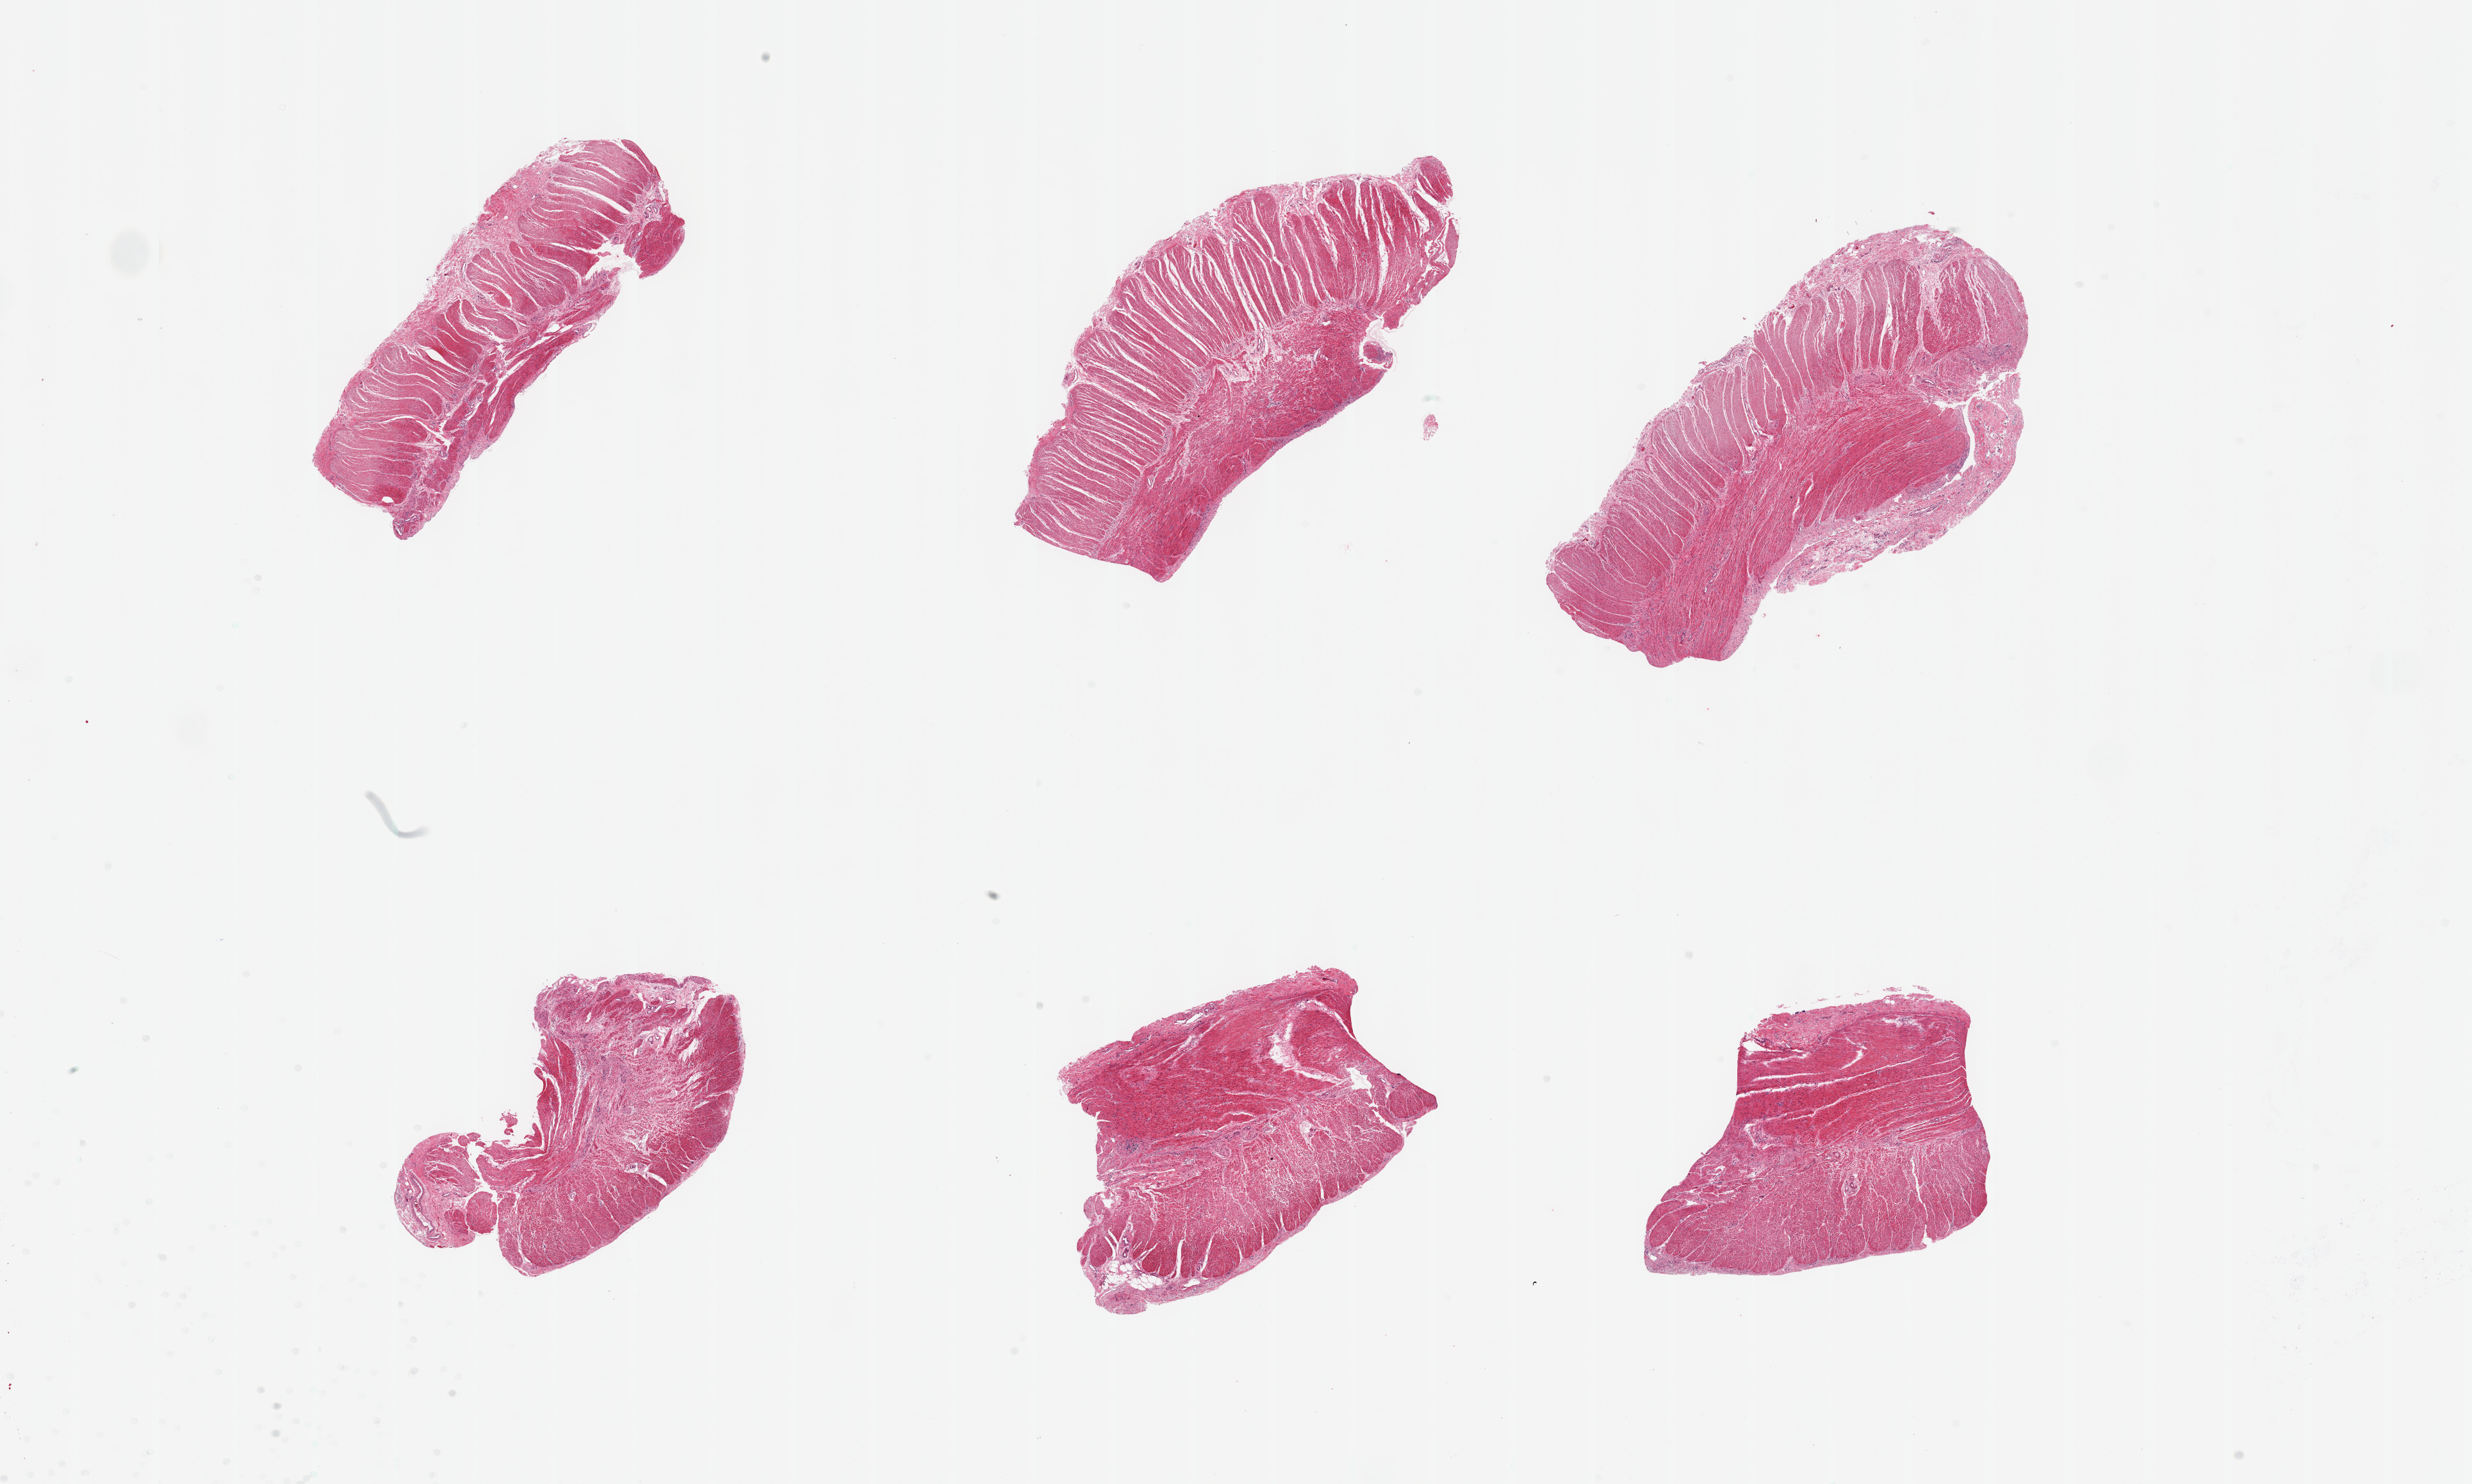
Digitized hematoxylin and eosin (H&E)-stained section — shown as a low-resolution overview of the whole scanned area (about 30.5 x 18.3 mm), PAXgene-fixed, paraffin-embedded tissue, sampled site (target tissue): sigmoid colon, donor tissue sample.
• reviewer comment on this tissue sample: 6 pieces; well trimmed muscularis